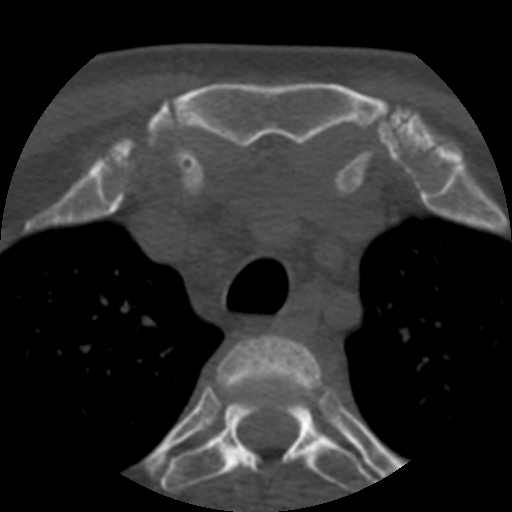
CT including the spine, one axial slice. Slice 420 of 508 in the series (ordered by position). 120 kVp. Bone window (W 1800 / L 400 HU). 1.25 mm slice thickness. 512 × 512 image matrix, field of view 160 × 160 mm. Patient age 57 years. From the clinical record (not read from this slice): primary cancer: prostate.
Outlined on this slice (semi-automatically segmented with operator editing):
- T2 vertebra: bounding box (x1, y1, x2, y2) in pixels: (217, 334, 324, 396)
- T3 vertebra: (162, 394, 377, 491)